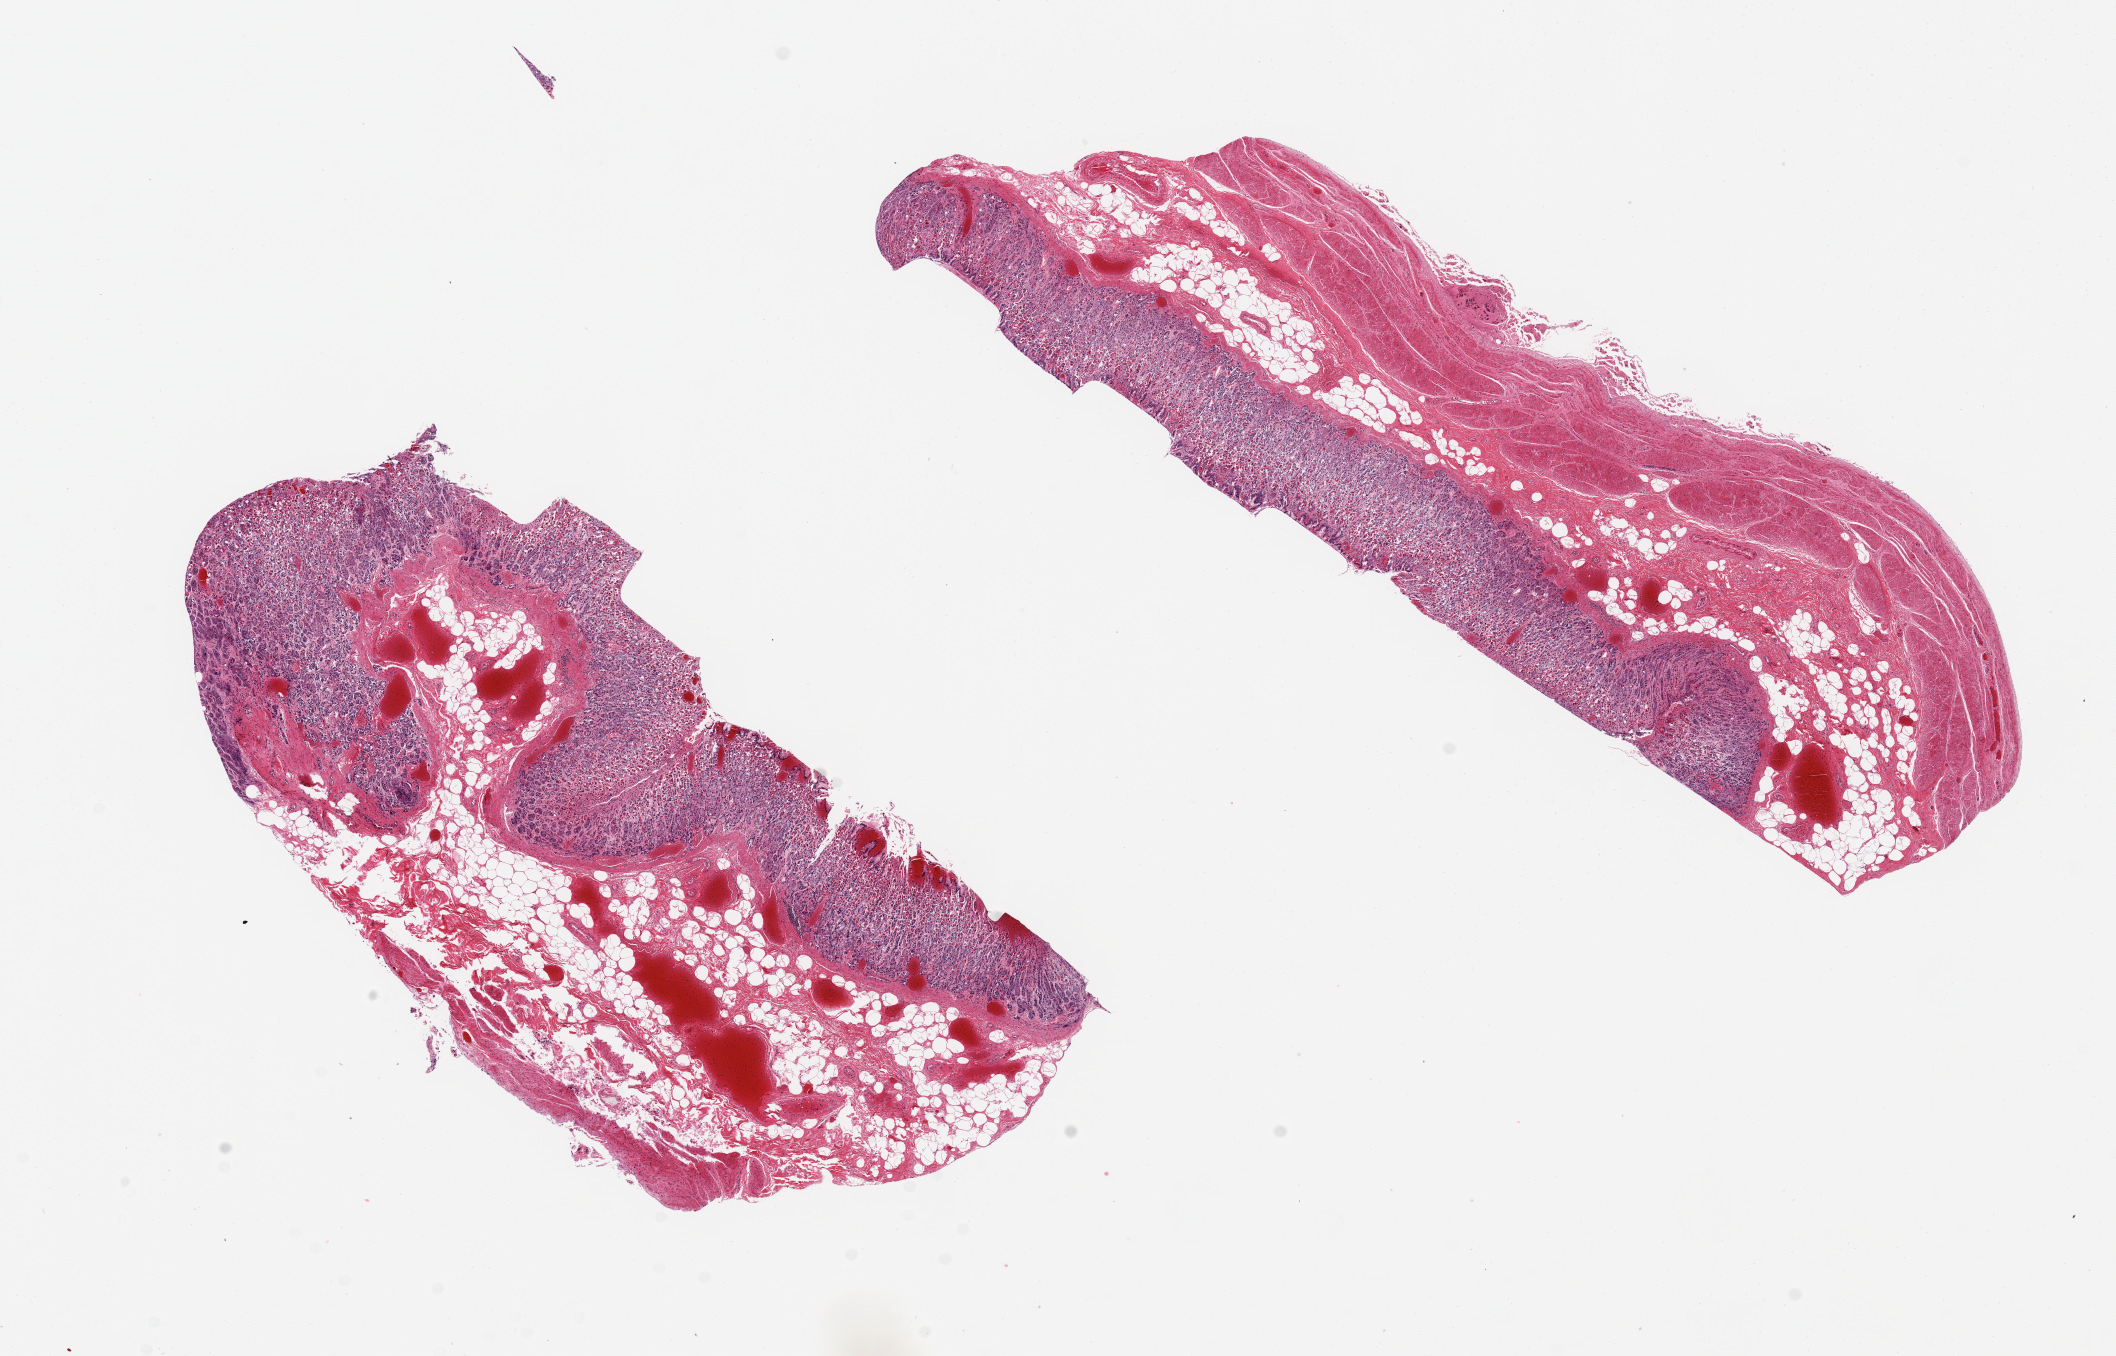
H&E whole-slide image, low-resolution overview of the scanned area, about 16.7 x 10.7 mm; PAXgene-fixed paraffin-embedded (PFPE) section; sampled site (target tissue): stomach; tissue donor sample. Female donor.
Pathologist's review note for this sample: 2 aliquots, ~8.5x2.5mm. Mucosa better preserved than usual for an autopsy, ~50% of thickness.